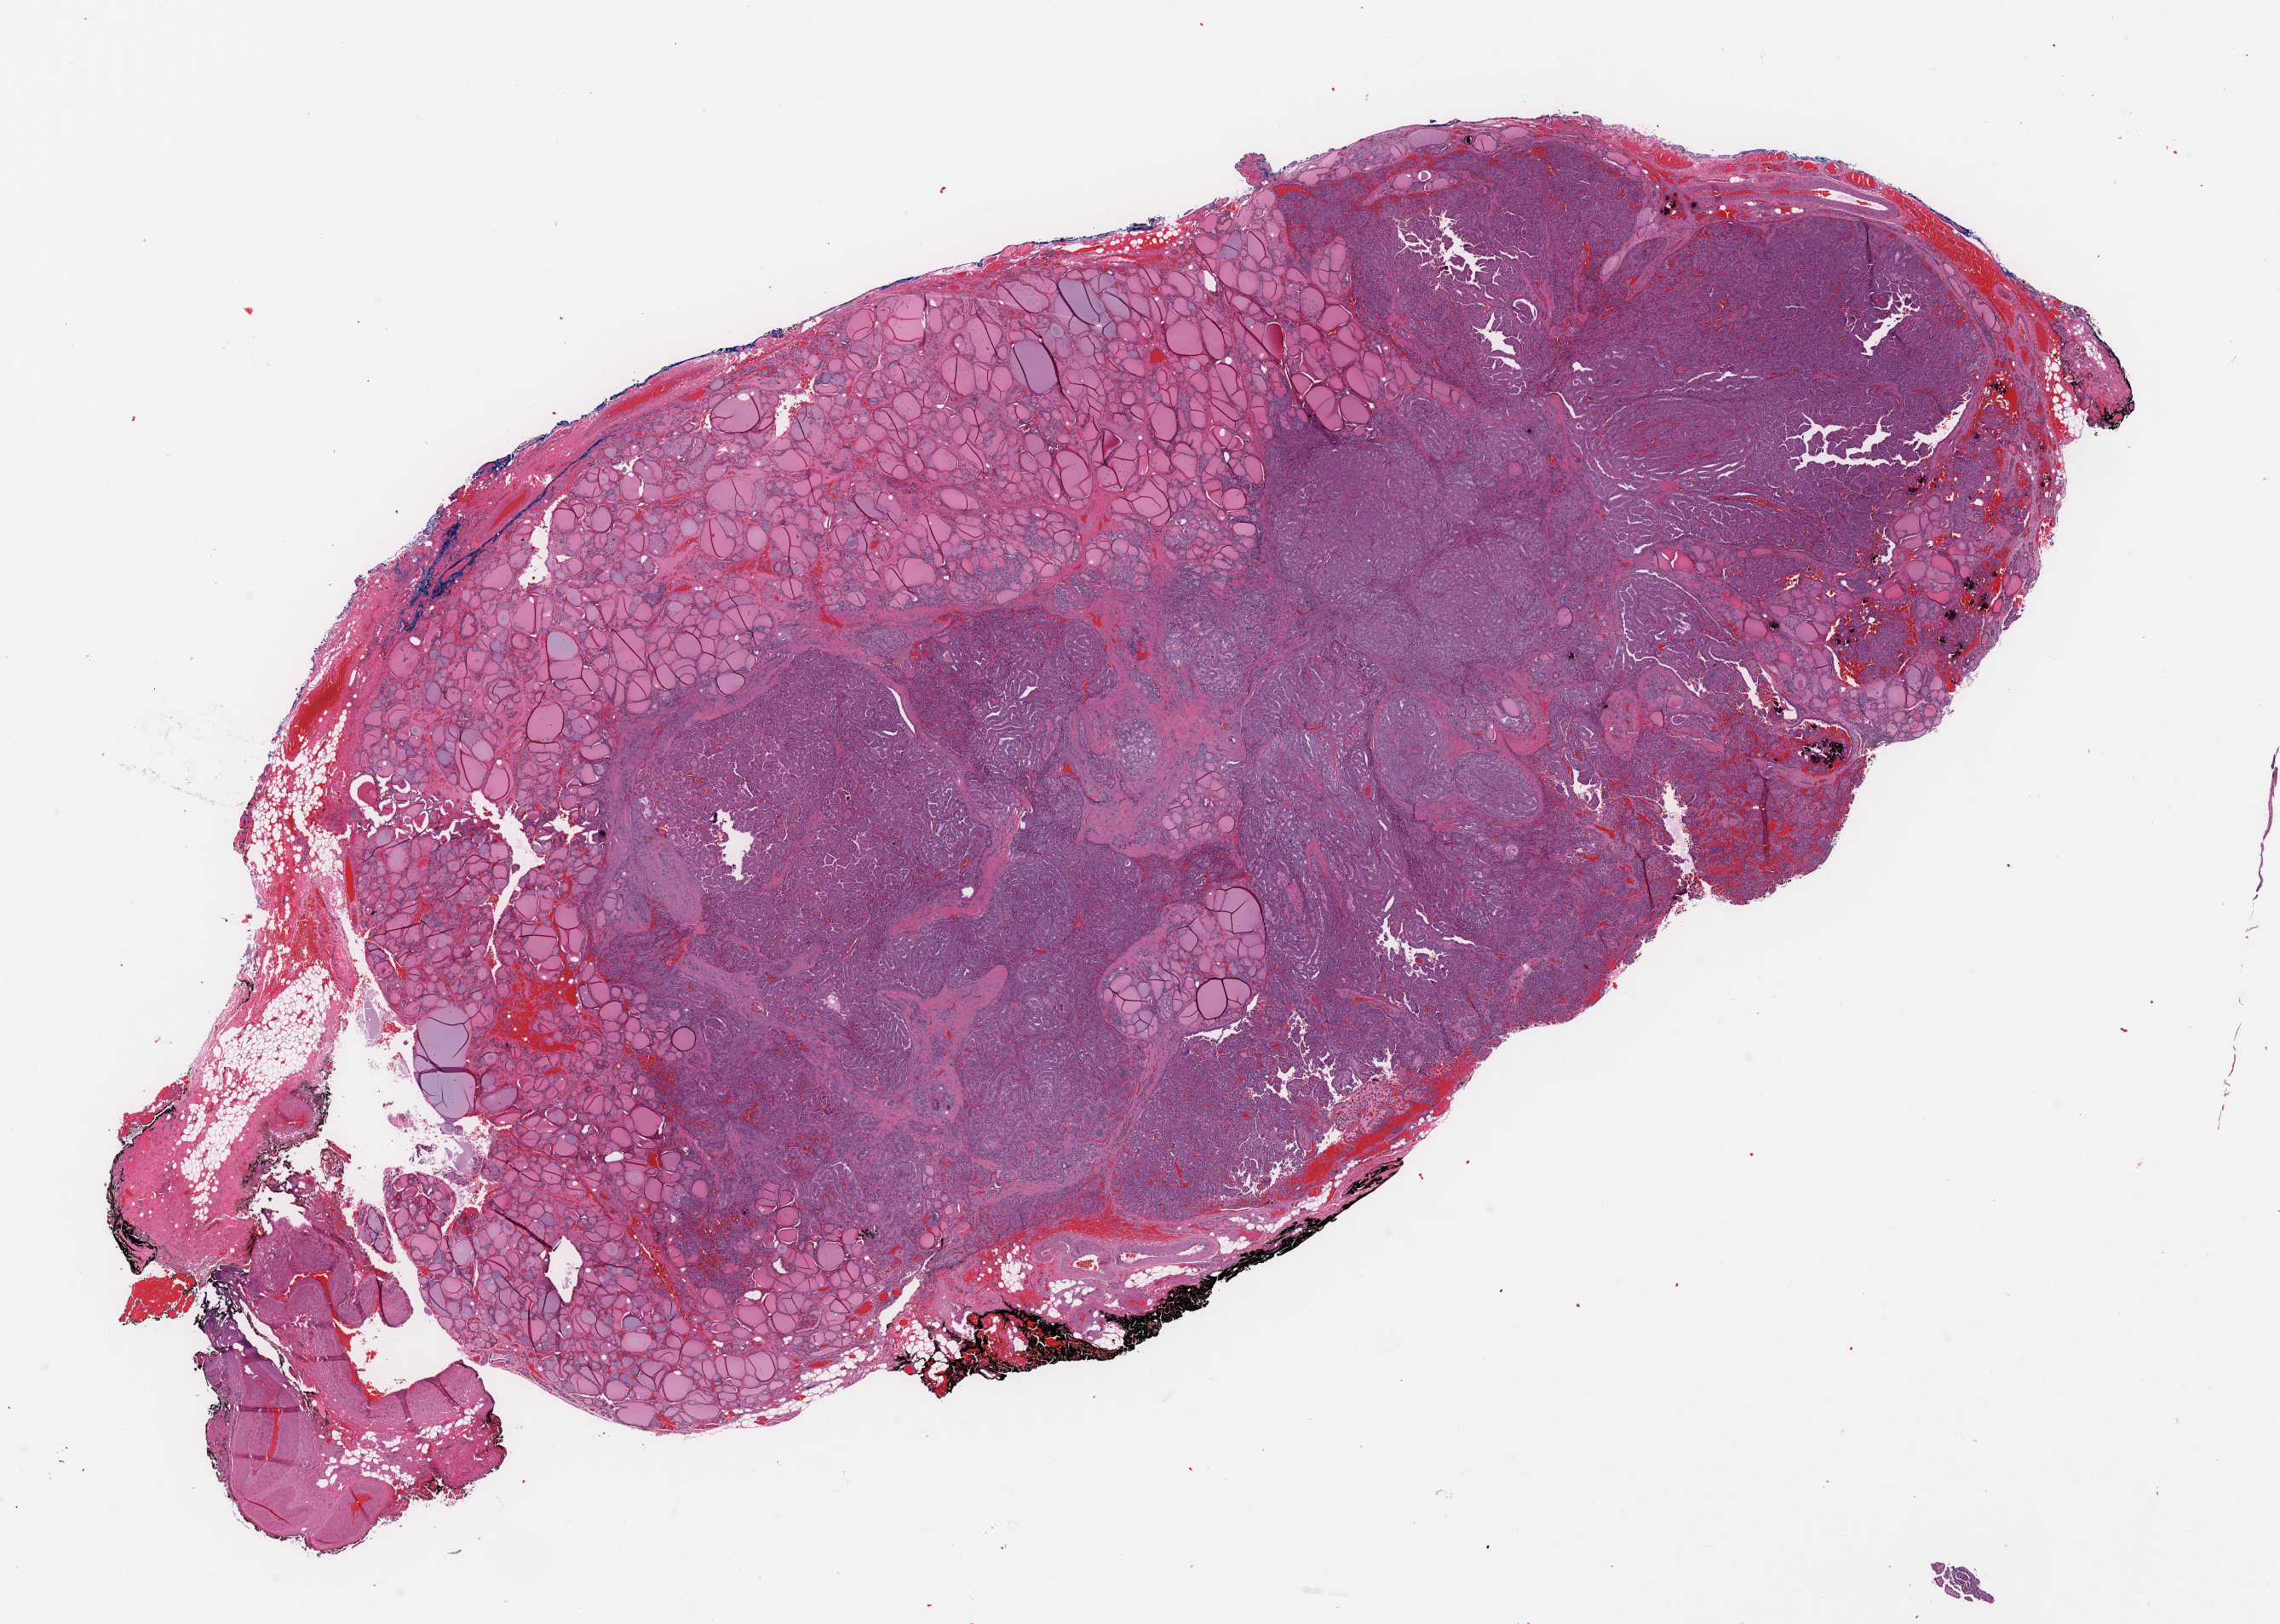
H&E-stained whole-slide image — low-resolution overview of the scanned area, about 21.1 x 15.0 mm (slide scanned at 40x). Formalin-fixed paraffin-embedded (FFPE) diagnostic section. Thyroid, primary tumour sample. Male patient; age at initial diagnosis 54 years.
AJCC pathologic stage: III (7th edition). Pathologic diagnosis: Papillary carcinoma, columnar cell (thyroid gland).